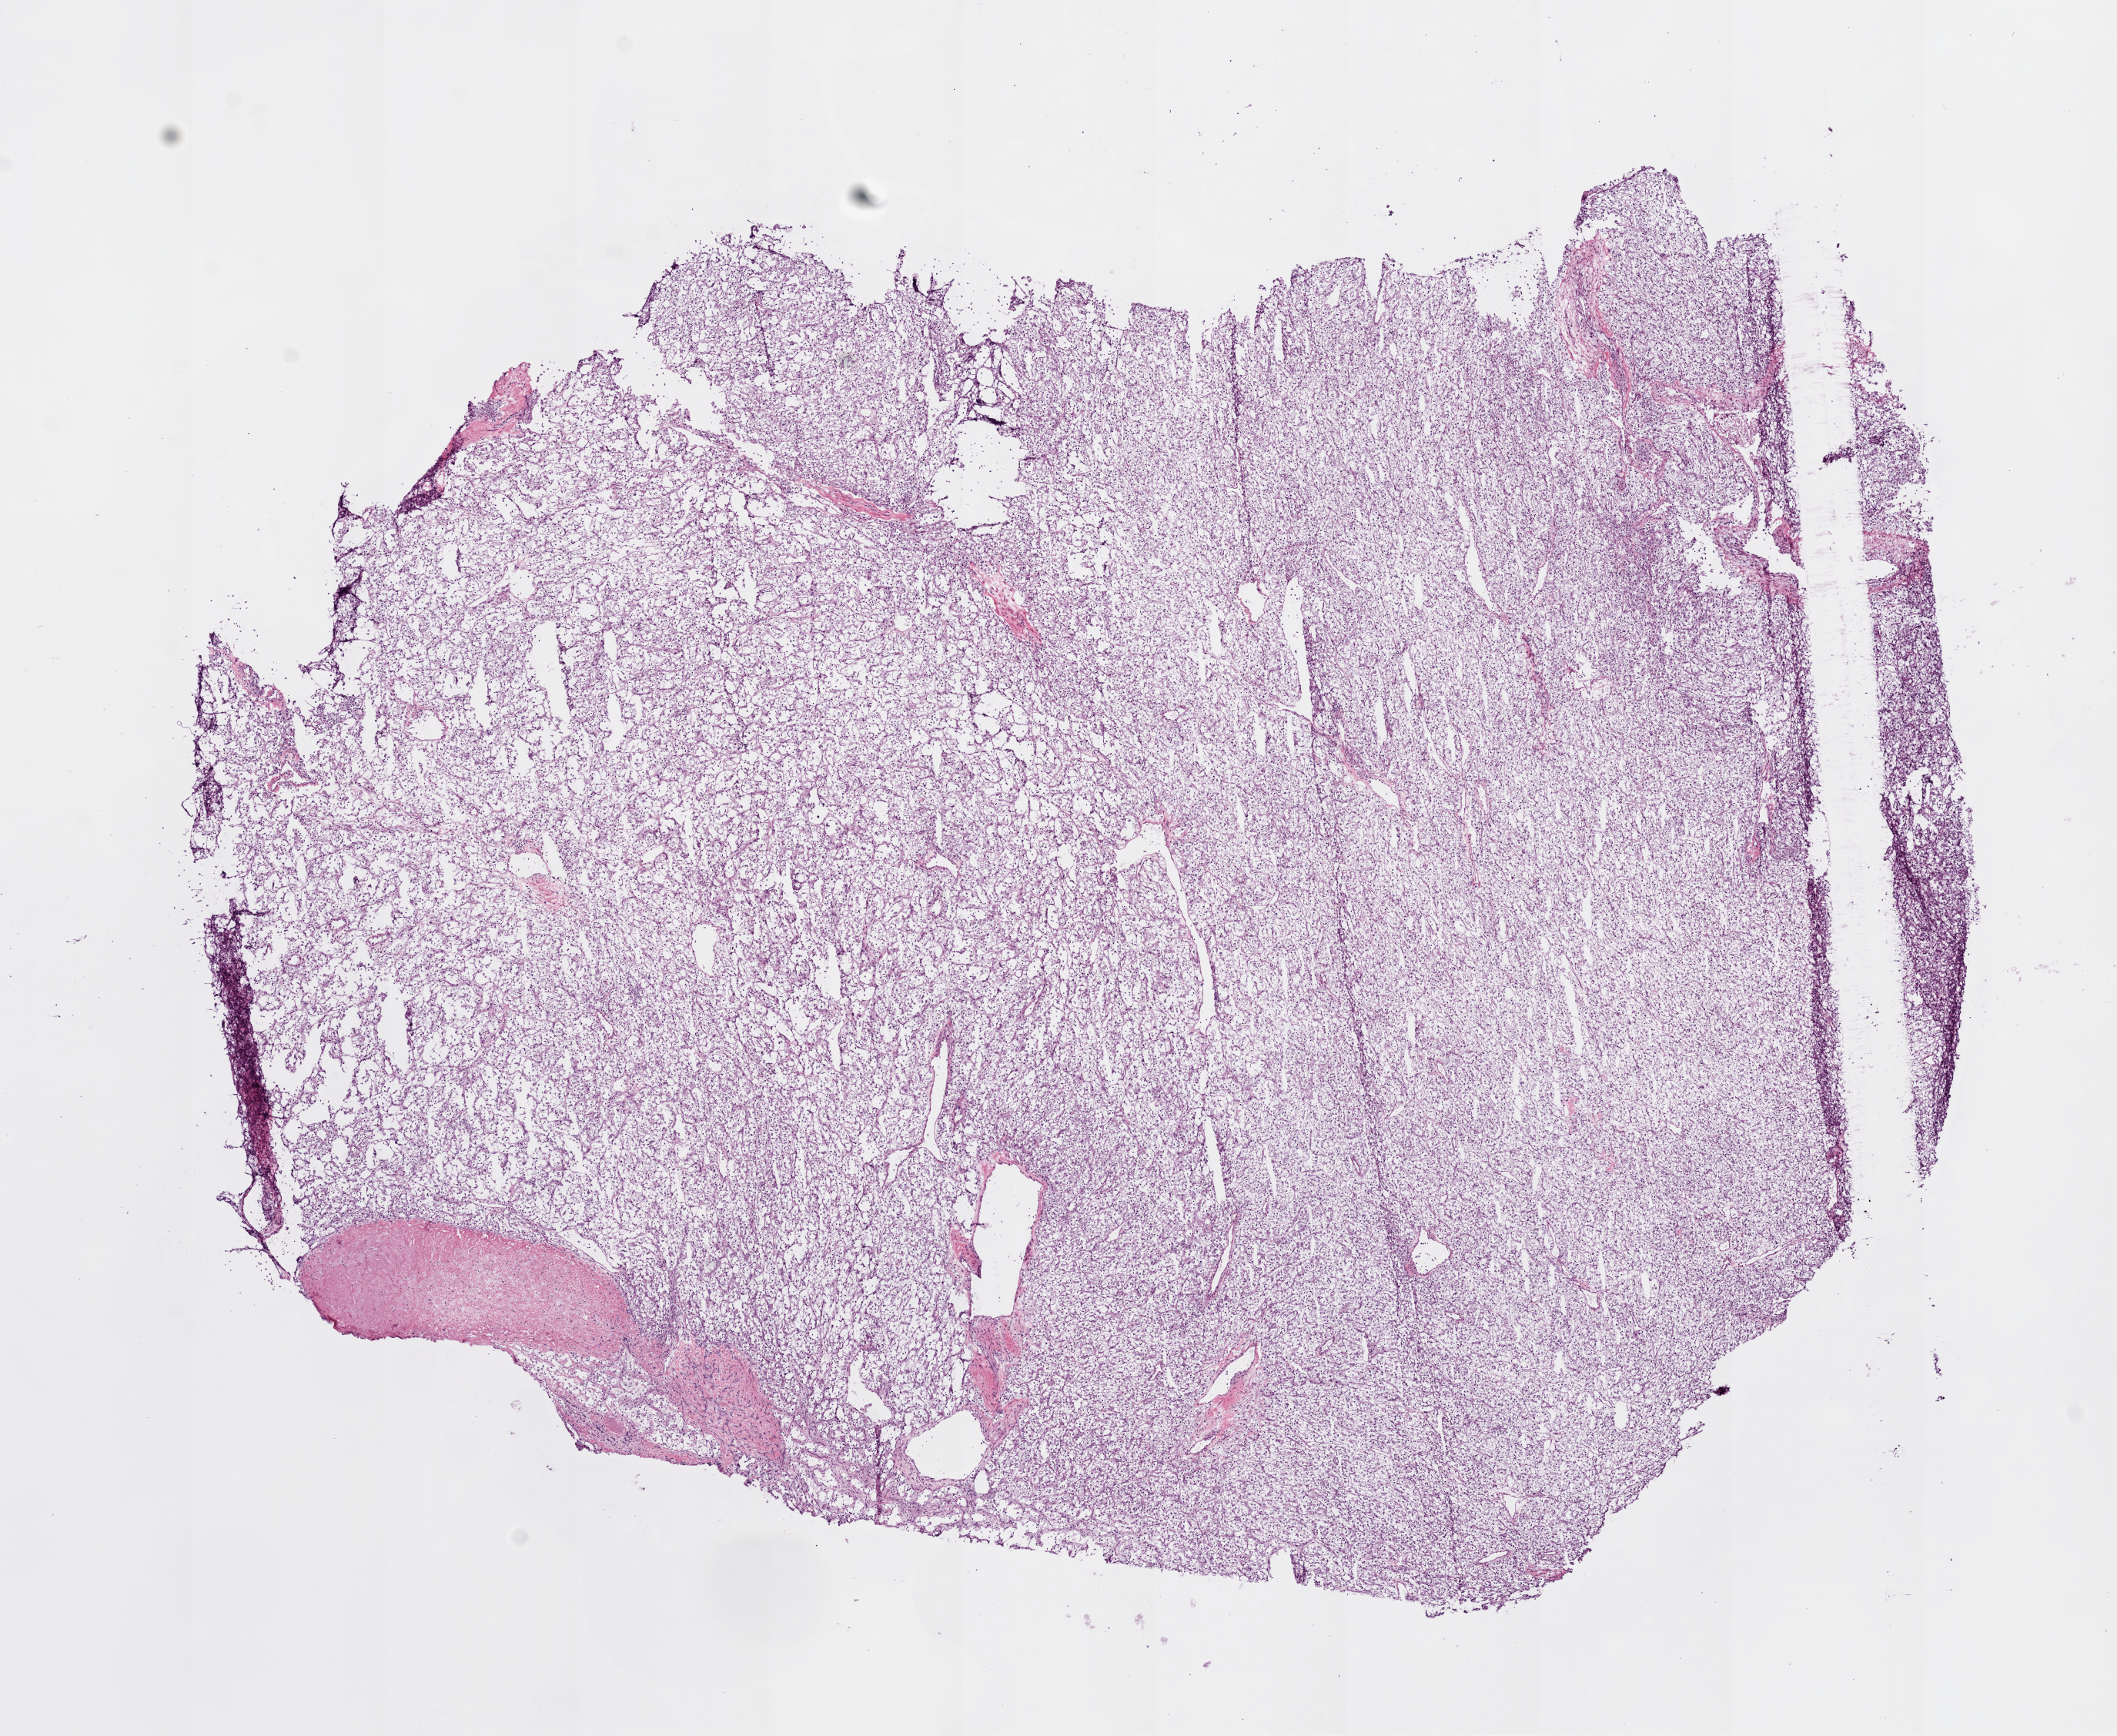
Whole-slide histology image, H&E, shown as a low-resolution overview of the whole scanned area (about 11.0 x 9.0 mm, slide scanned at 20x); frozen section from the bottom of the tissue portion; kidney, primary tumour sample. Male, age 56 years at initial diagnosis. Histologic grade: G2 (moderately differentiated). Pathologist review of this section (percent, as recorded): tumour cells 92%, tumour nuclei 90%, normal cells 0%, stromal cells 8%, necrosis 0%.
- AJCC pathologic stage: IV
- pathologic diagnosis: Clear cell adenocarcinoma, NOS